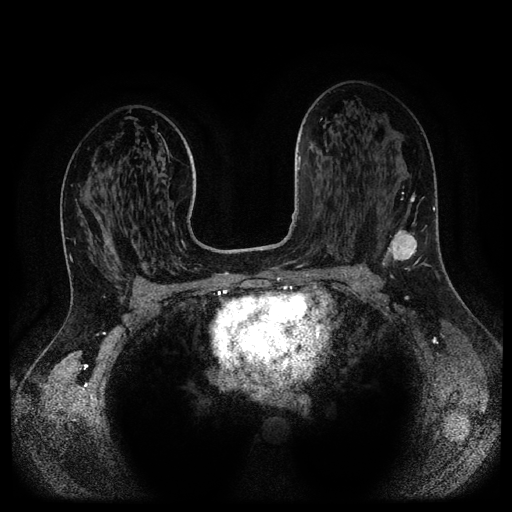
Breast MRI (dynamic contrast-enhanced, multi-phase), one axial slice; position 65 of 116 along the scan axis; dynamic contrast-enhanced series, time point 2 of 5 at this slice position (early post-contrast); 1.5 T; TE 2.6 ms, TR 5.3 ms; 2.1 mm slice thickness; 512 × 512 image matrix. Female patient, age 37 years.
Outlined on this slice (semi-automatically segmented with operator editing):
- breast lesion (labelled 'tumour' in the annotation; benign lesions carry a separate 'benign' label): bounding box [x1, y1, x2, y2] px = [382, 192, 428, 268]